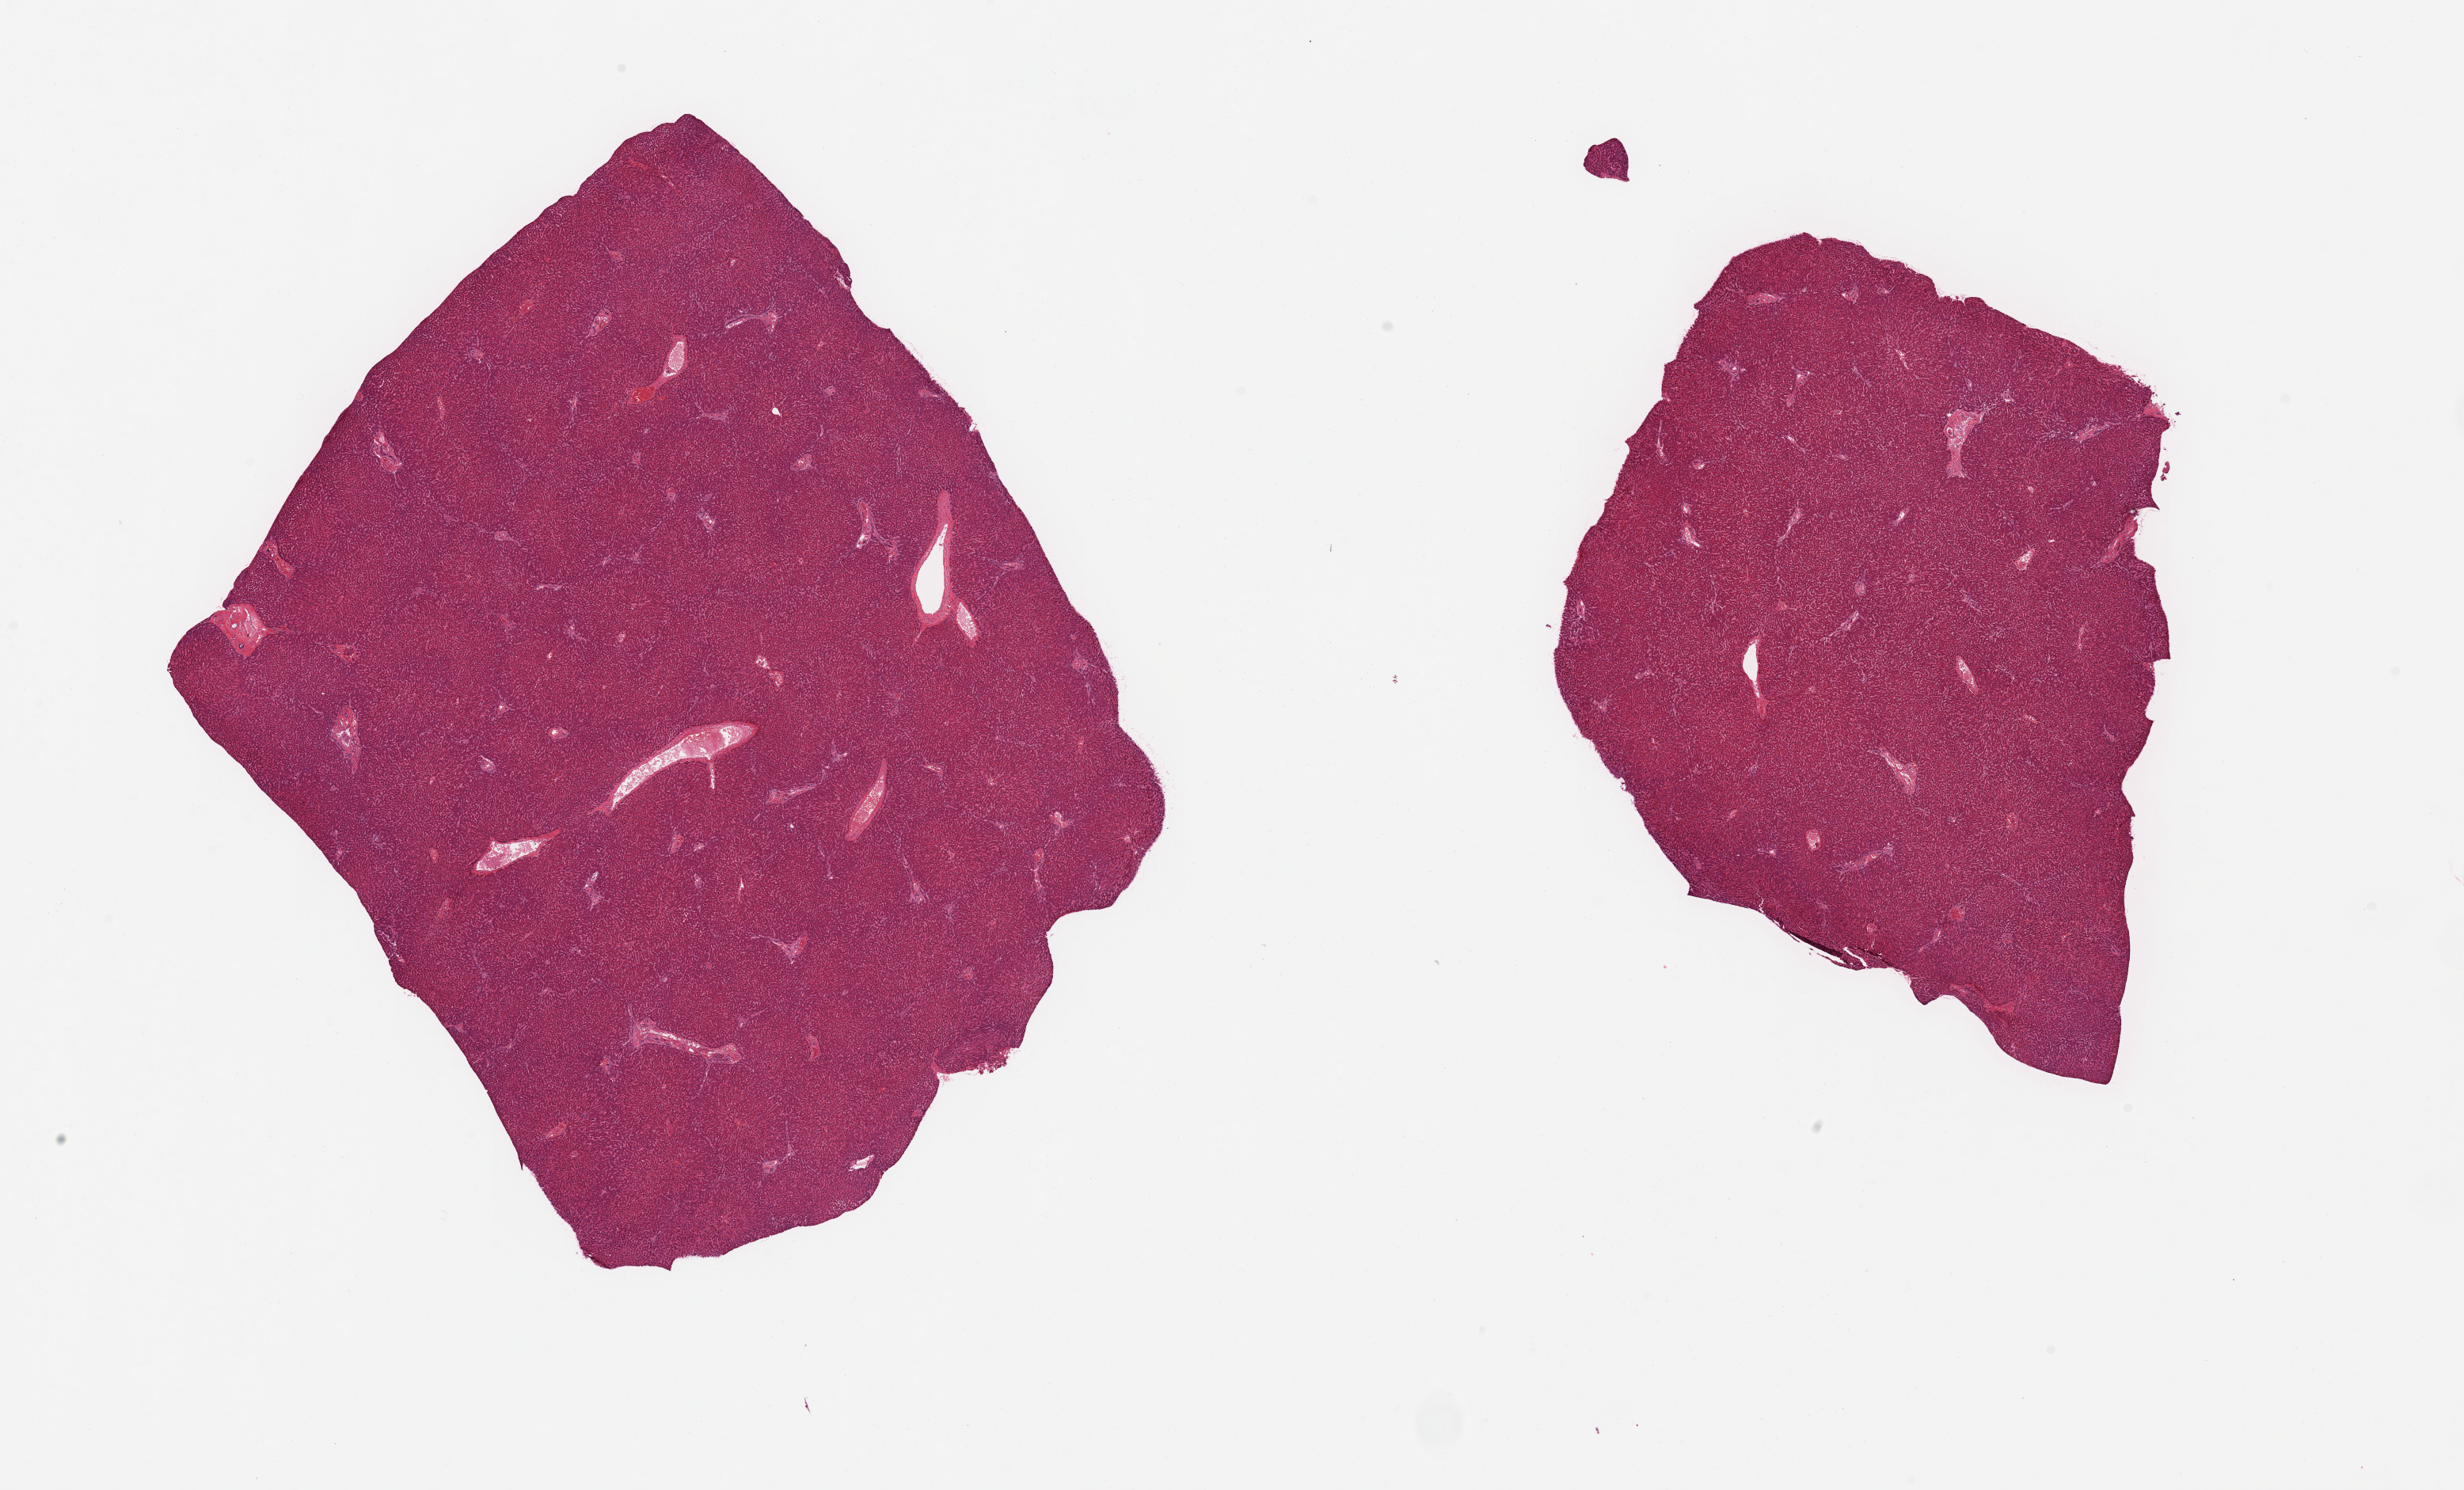
Whole-slide image, haematoxylin and eosin stain, brightfield — shown as a low-resolution overview of the whole scanned area (about 24.6 x 14.9 mm). PAXgene-fixed paraffin-embedded (PFPE) section. Section of liver (target tissue). Donor tissue sample. Donor sex: male.
Reviewer comment on this tissue sample: 2 pieces, no abnormalities.